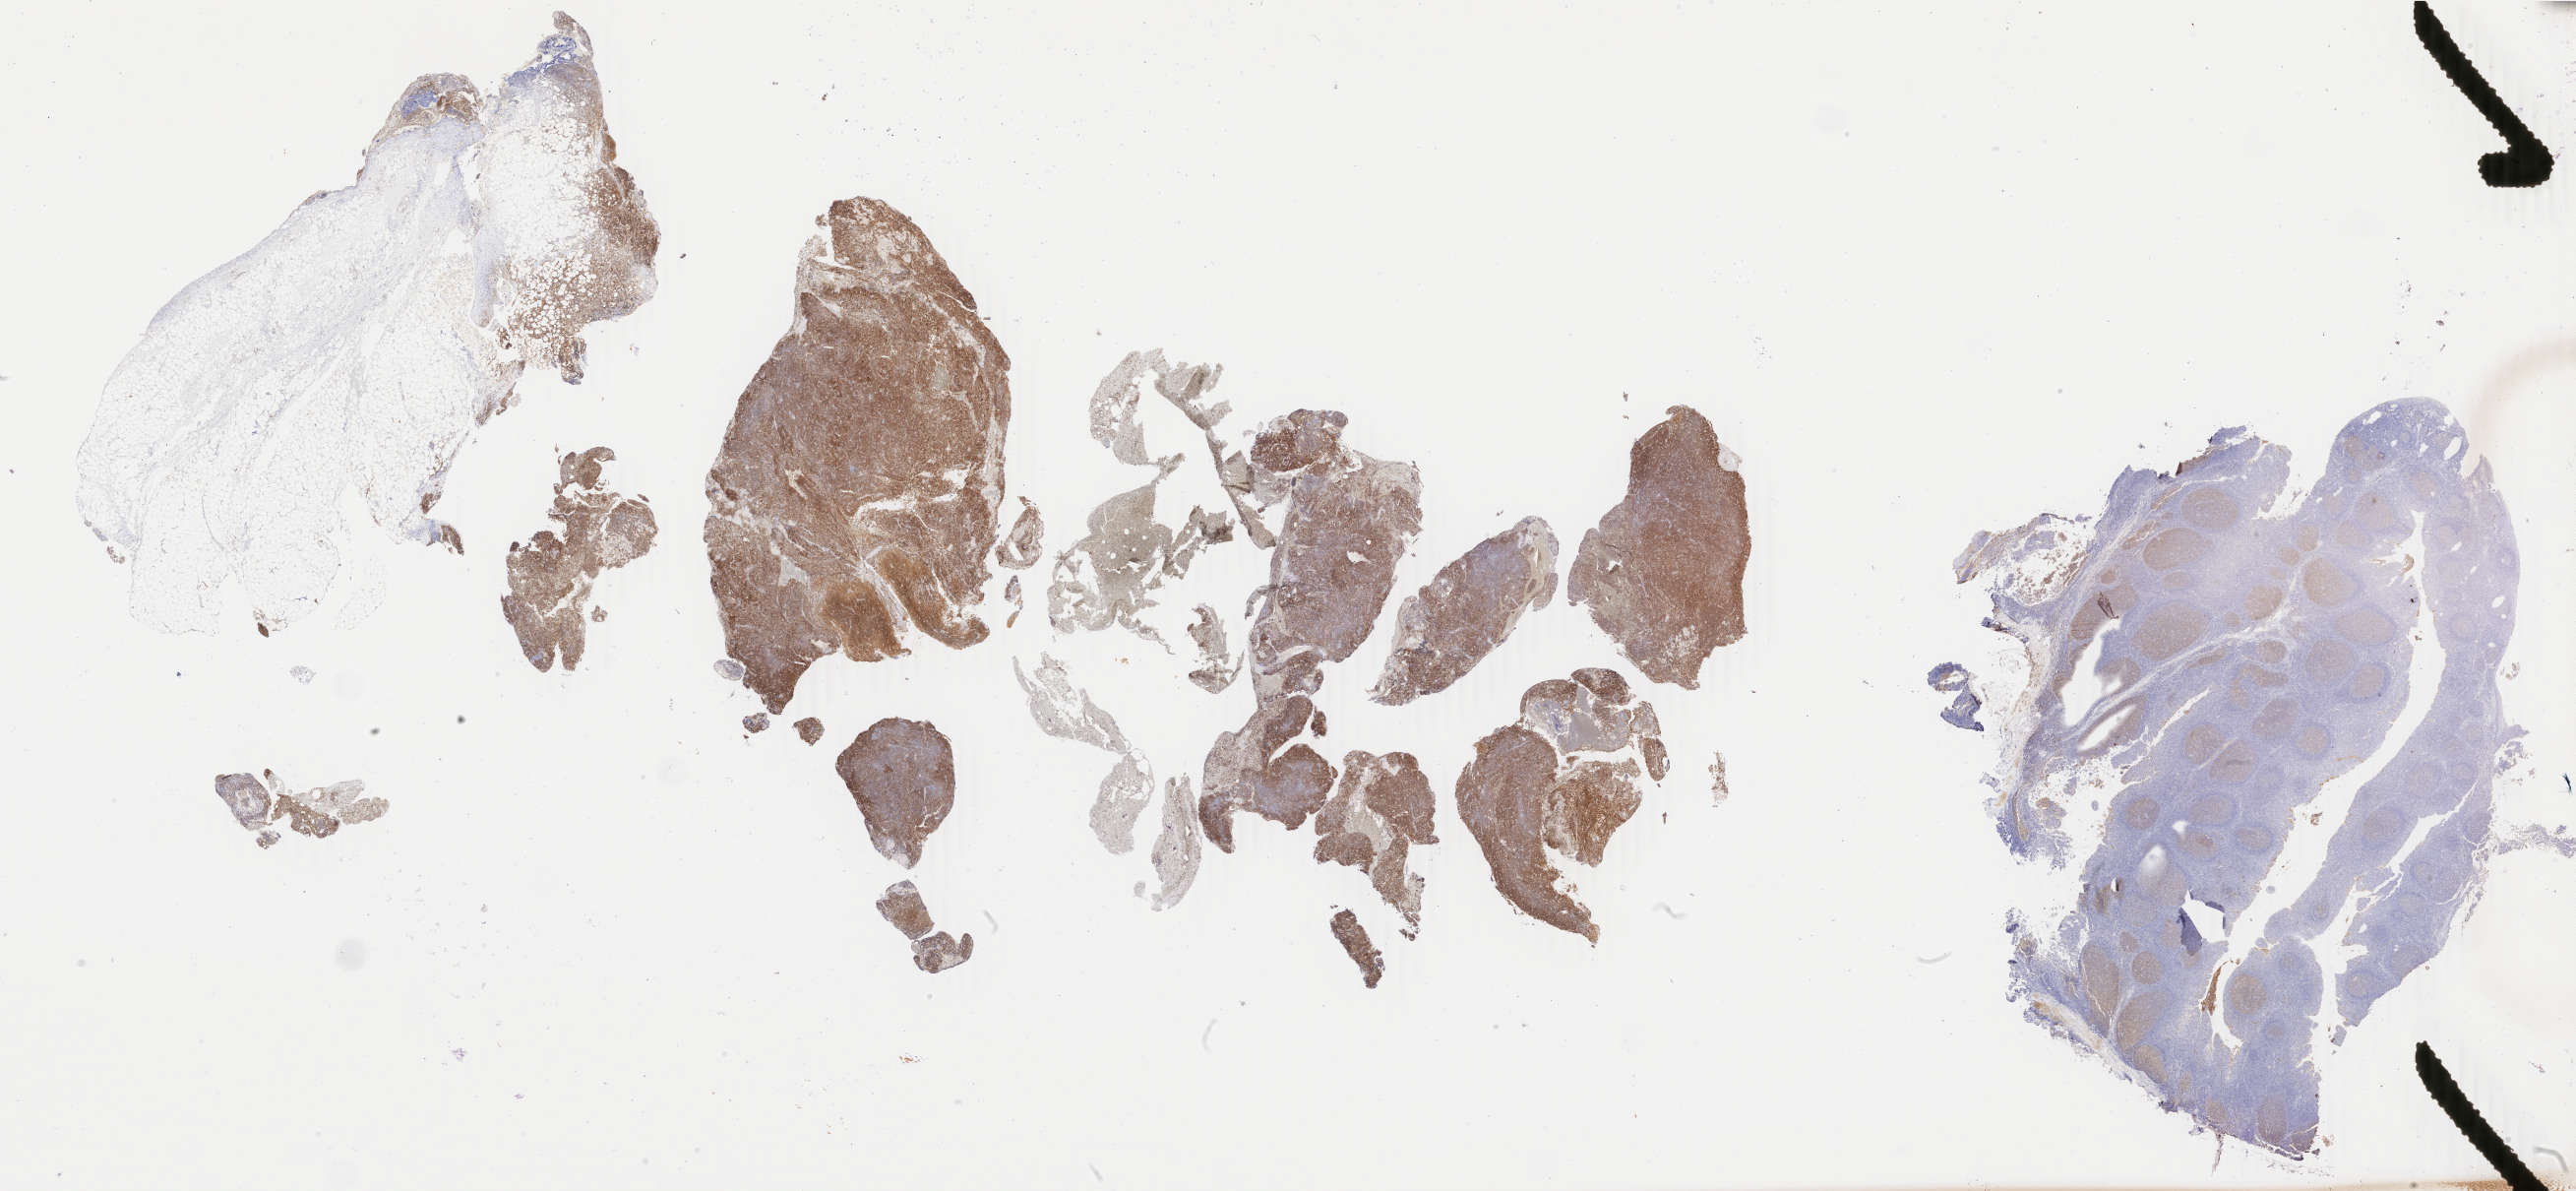
Whole-slide image, immunohistochemical stain for CD10, whole scanned area (about 41.6 x 19.2 mm) shown as a low-resolution overview, tumor tissue, anatomic site: abdominal lymph node. Patient male; 27 years old.
Histologic diagnosis: Burkitt lymphoma, NOS.